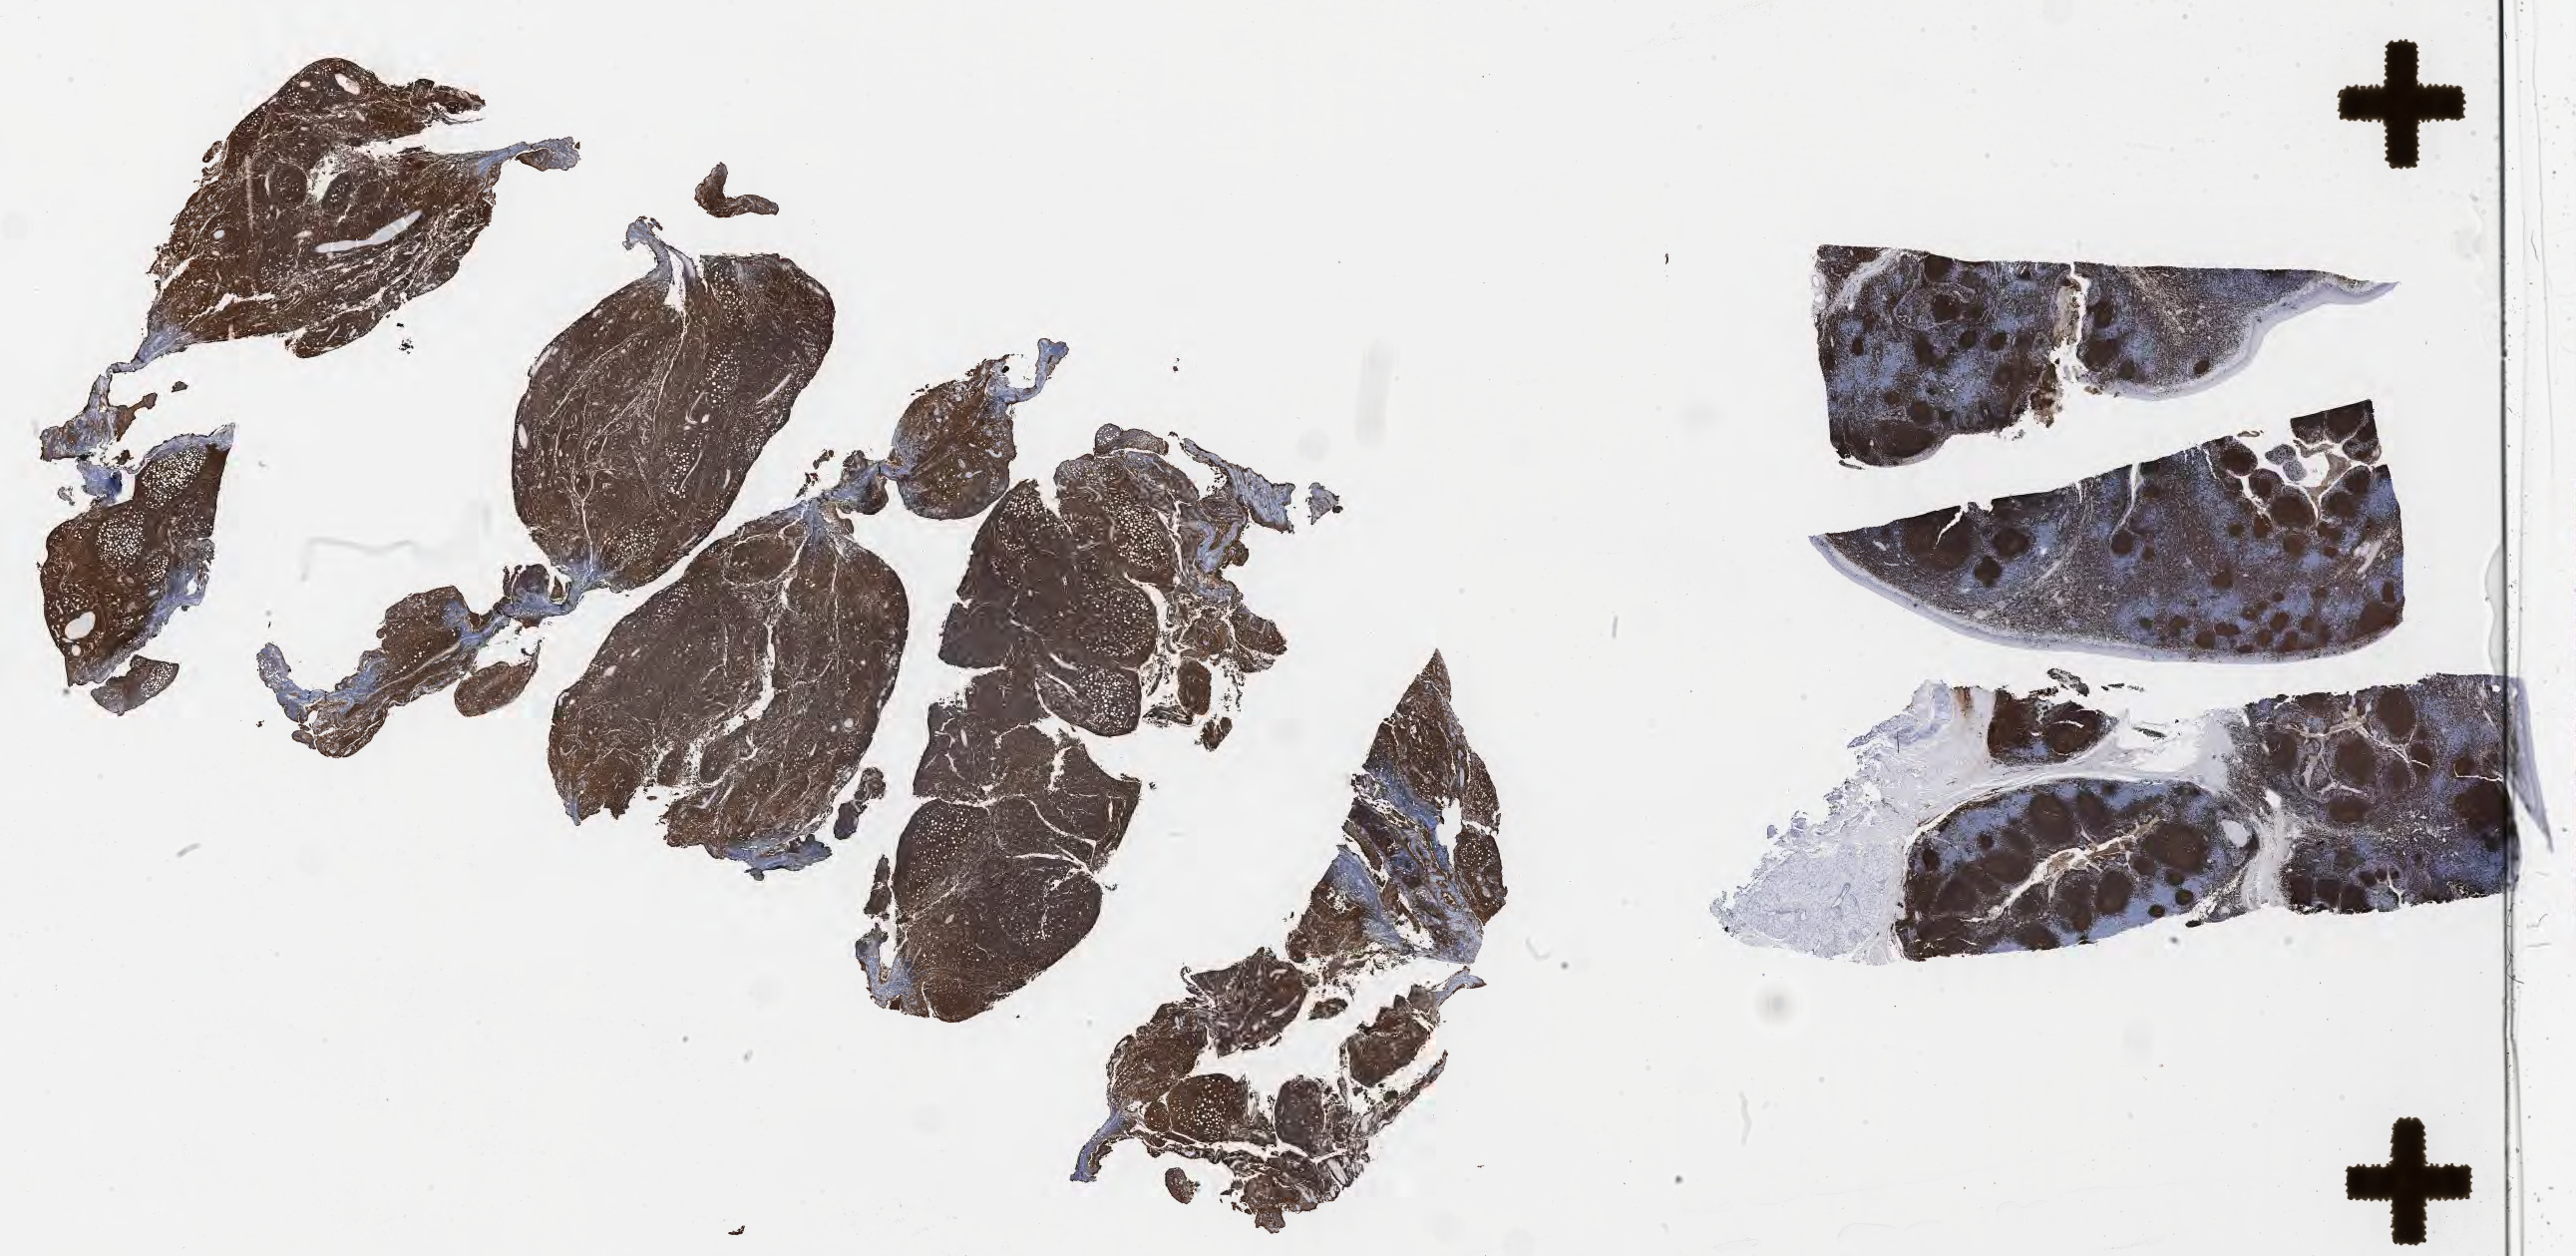
Immunohistochemistry (IHC) whole-slide image stained for CD20 — low-resolution overview of the scanned area, about 41.7 x 20.3 mm; tumor tissue; site: peritoneum. Patient: male, age at initial diagnosis 8 years.
• diagnosis: Burkitt lymphoma, NOS